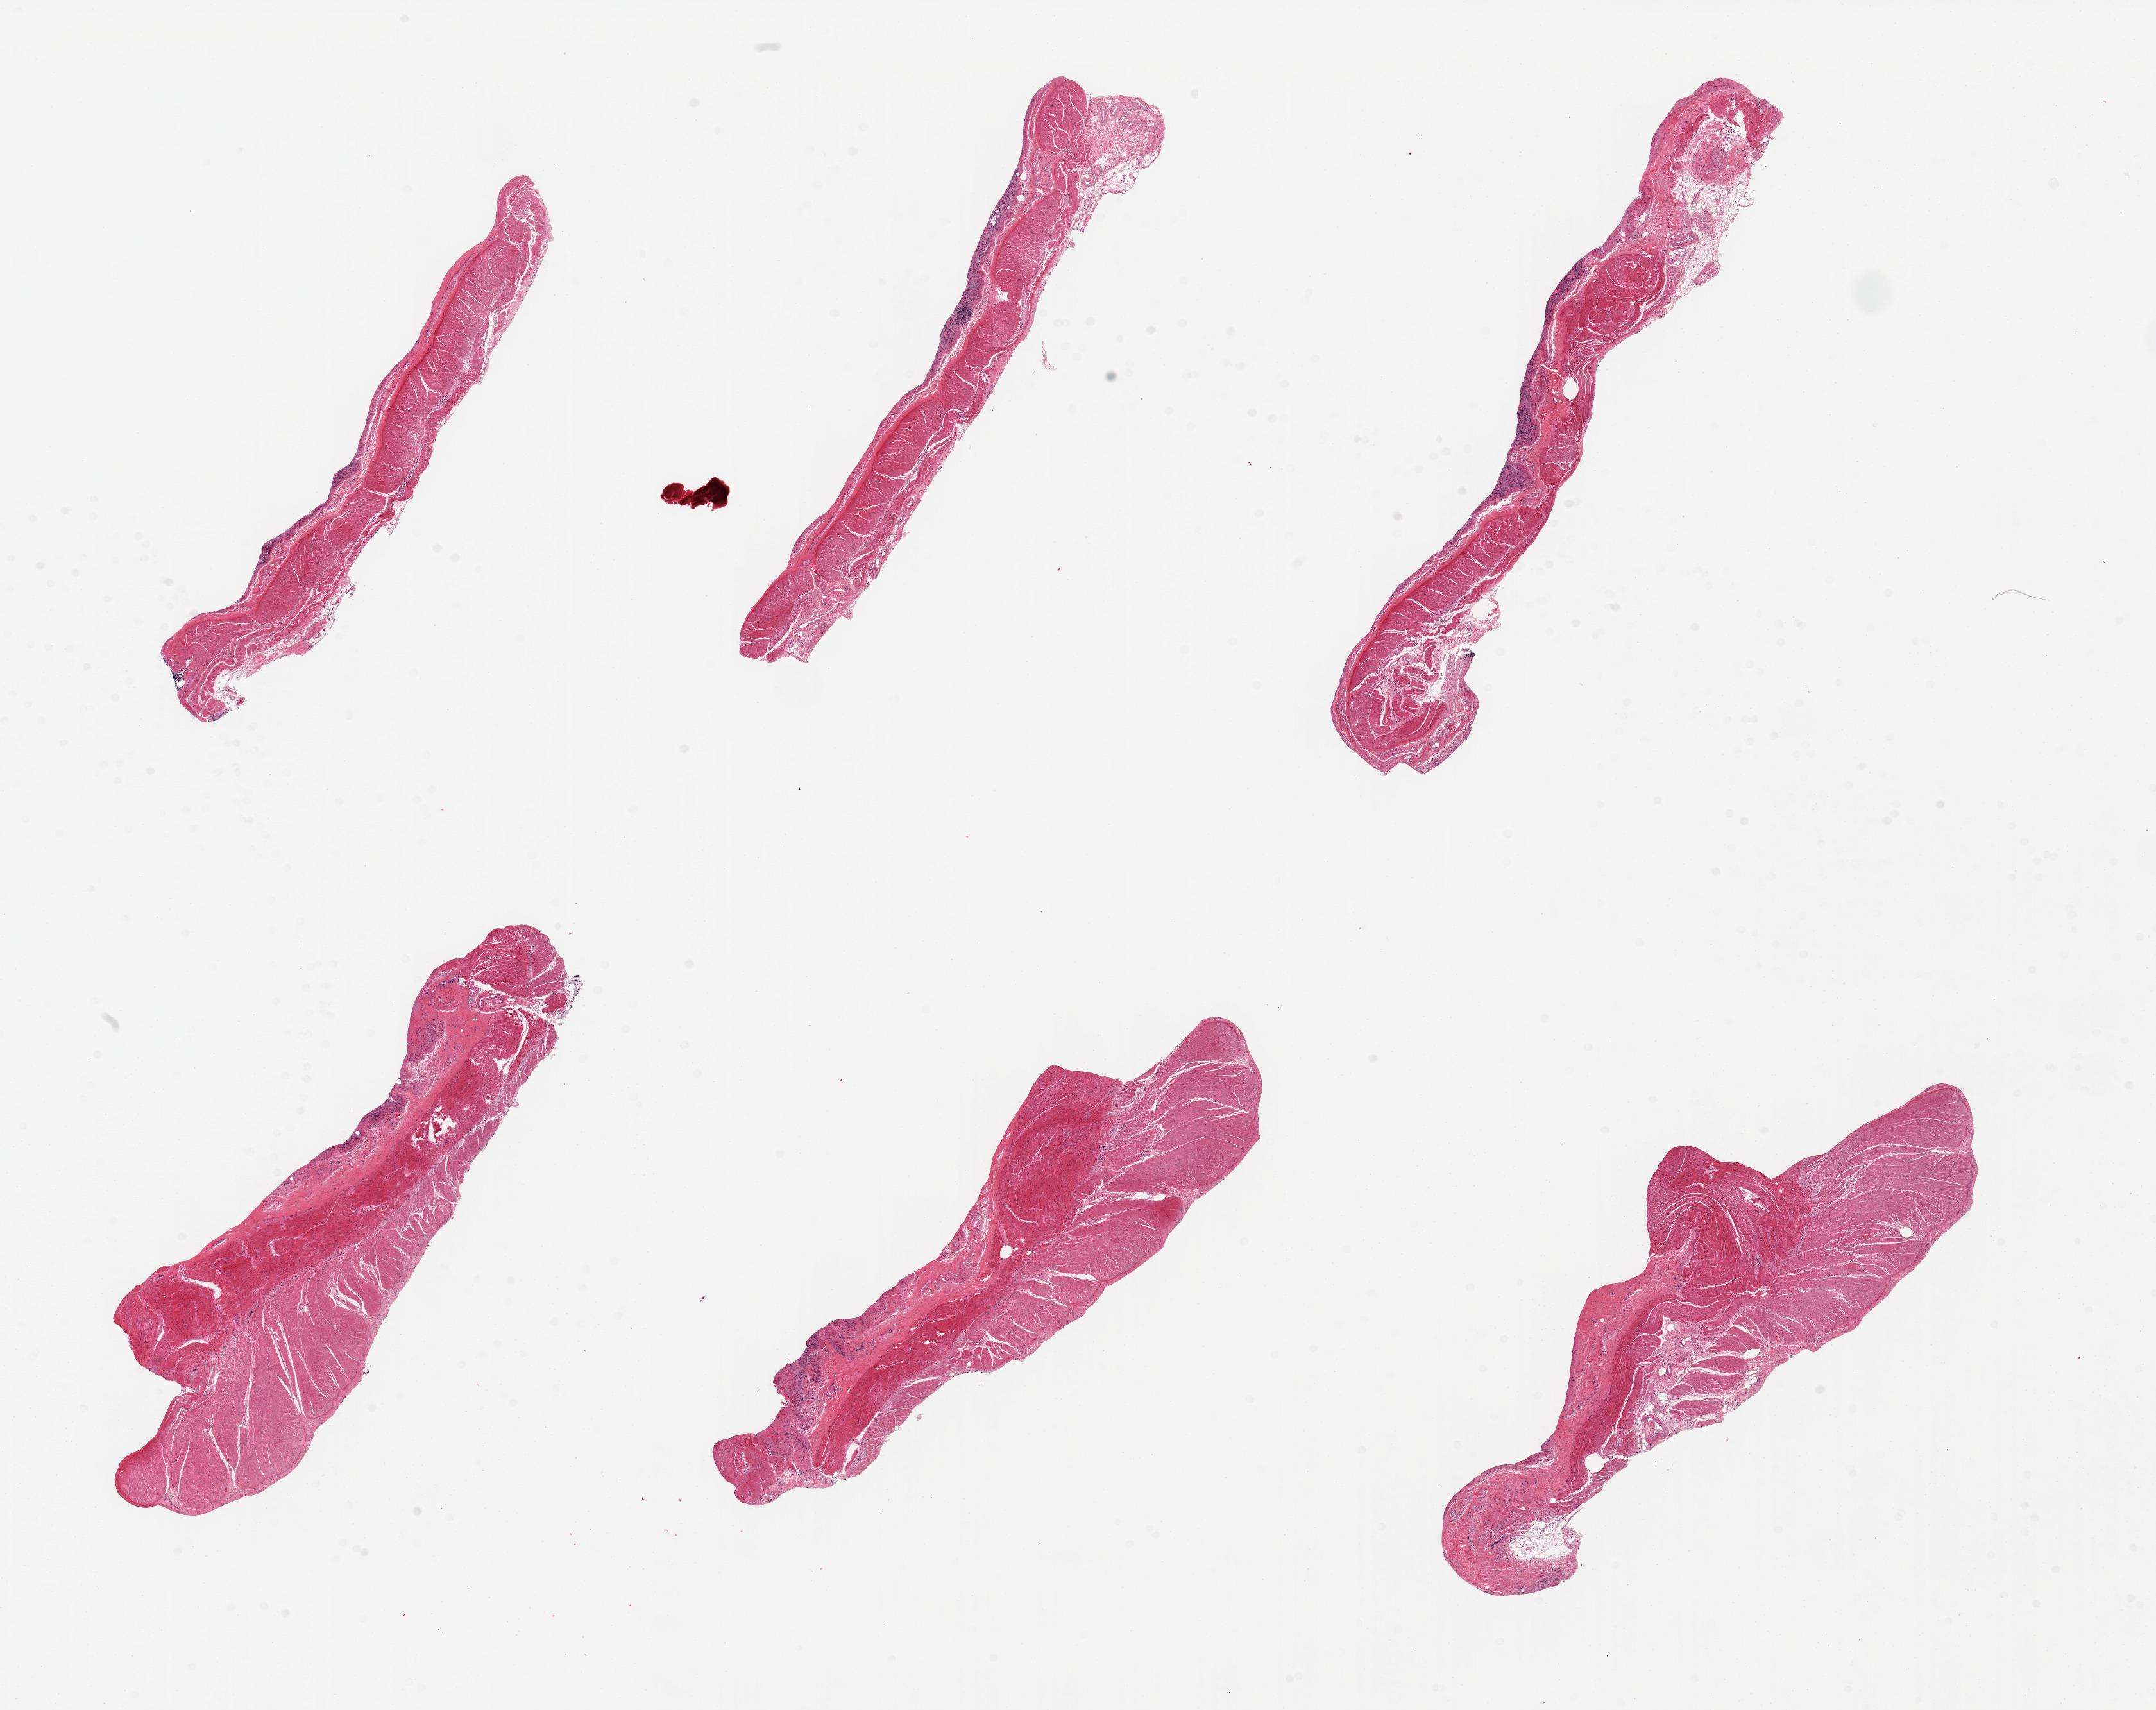
Whole-slide image, hematoxylin and eosin (H&E) stain, a low-resolution overview of the entire scanned area, about 26.6 x 21.1 mm (from a 20x scan); PAXgene-fixed, paraffin-embedded tissue; sampled site (target tissue): sigmoid colon; tissue donor sample. Male donor.
* reviewer comment on this tissue sample: 6 pieces, all muscularis (target)